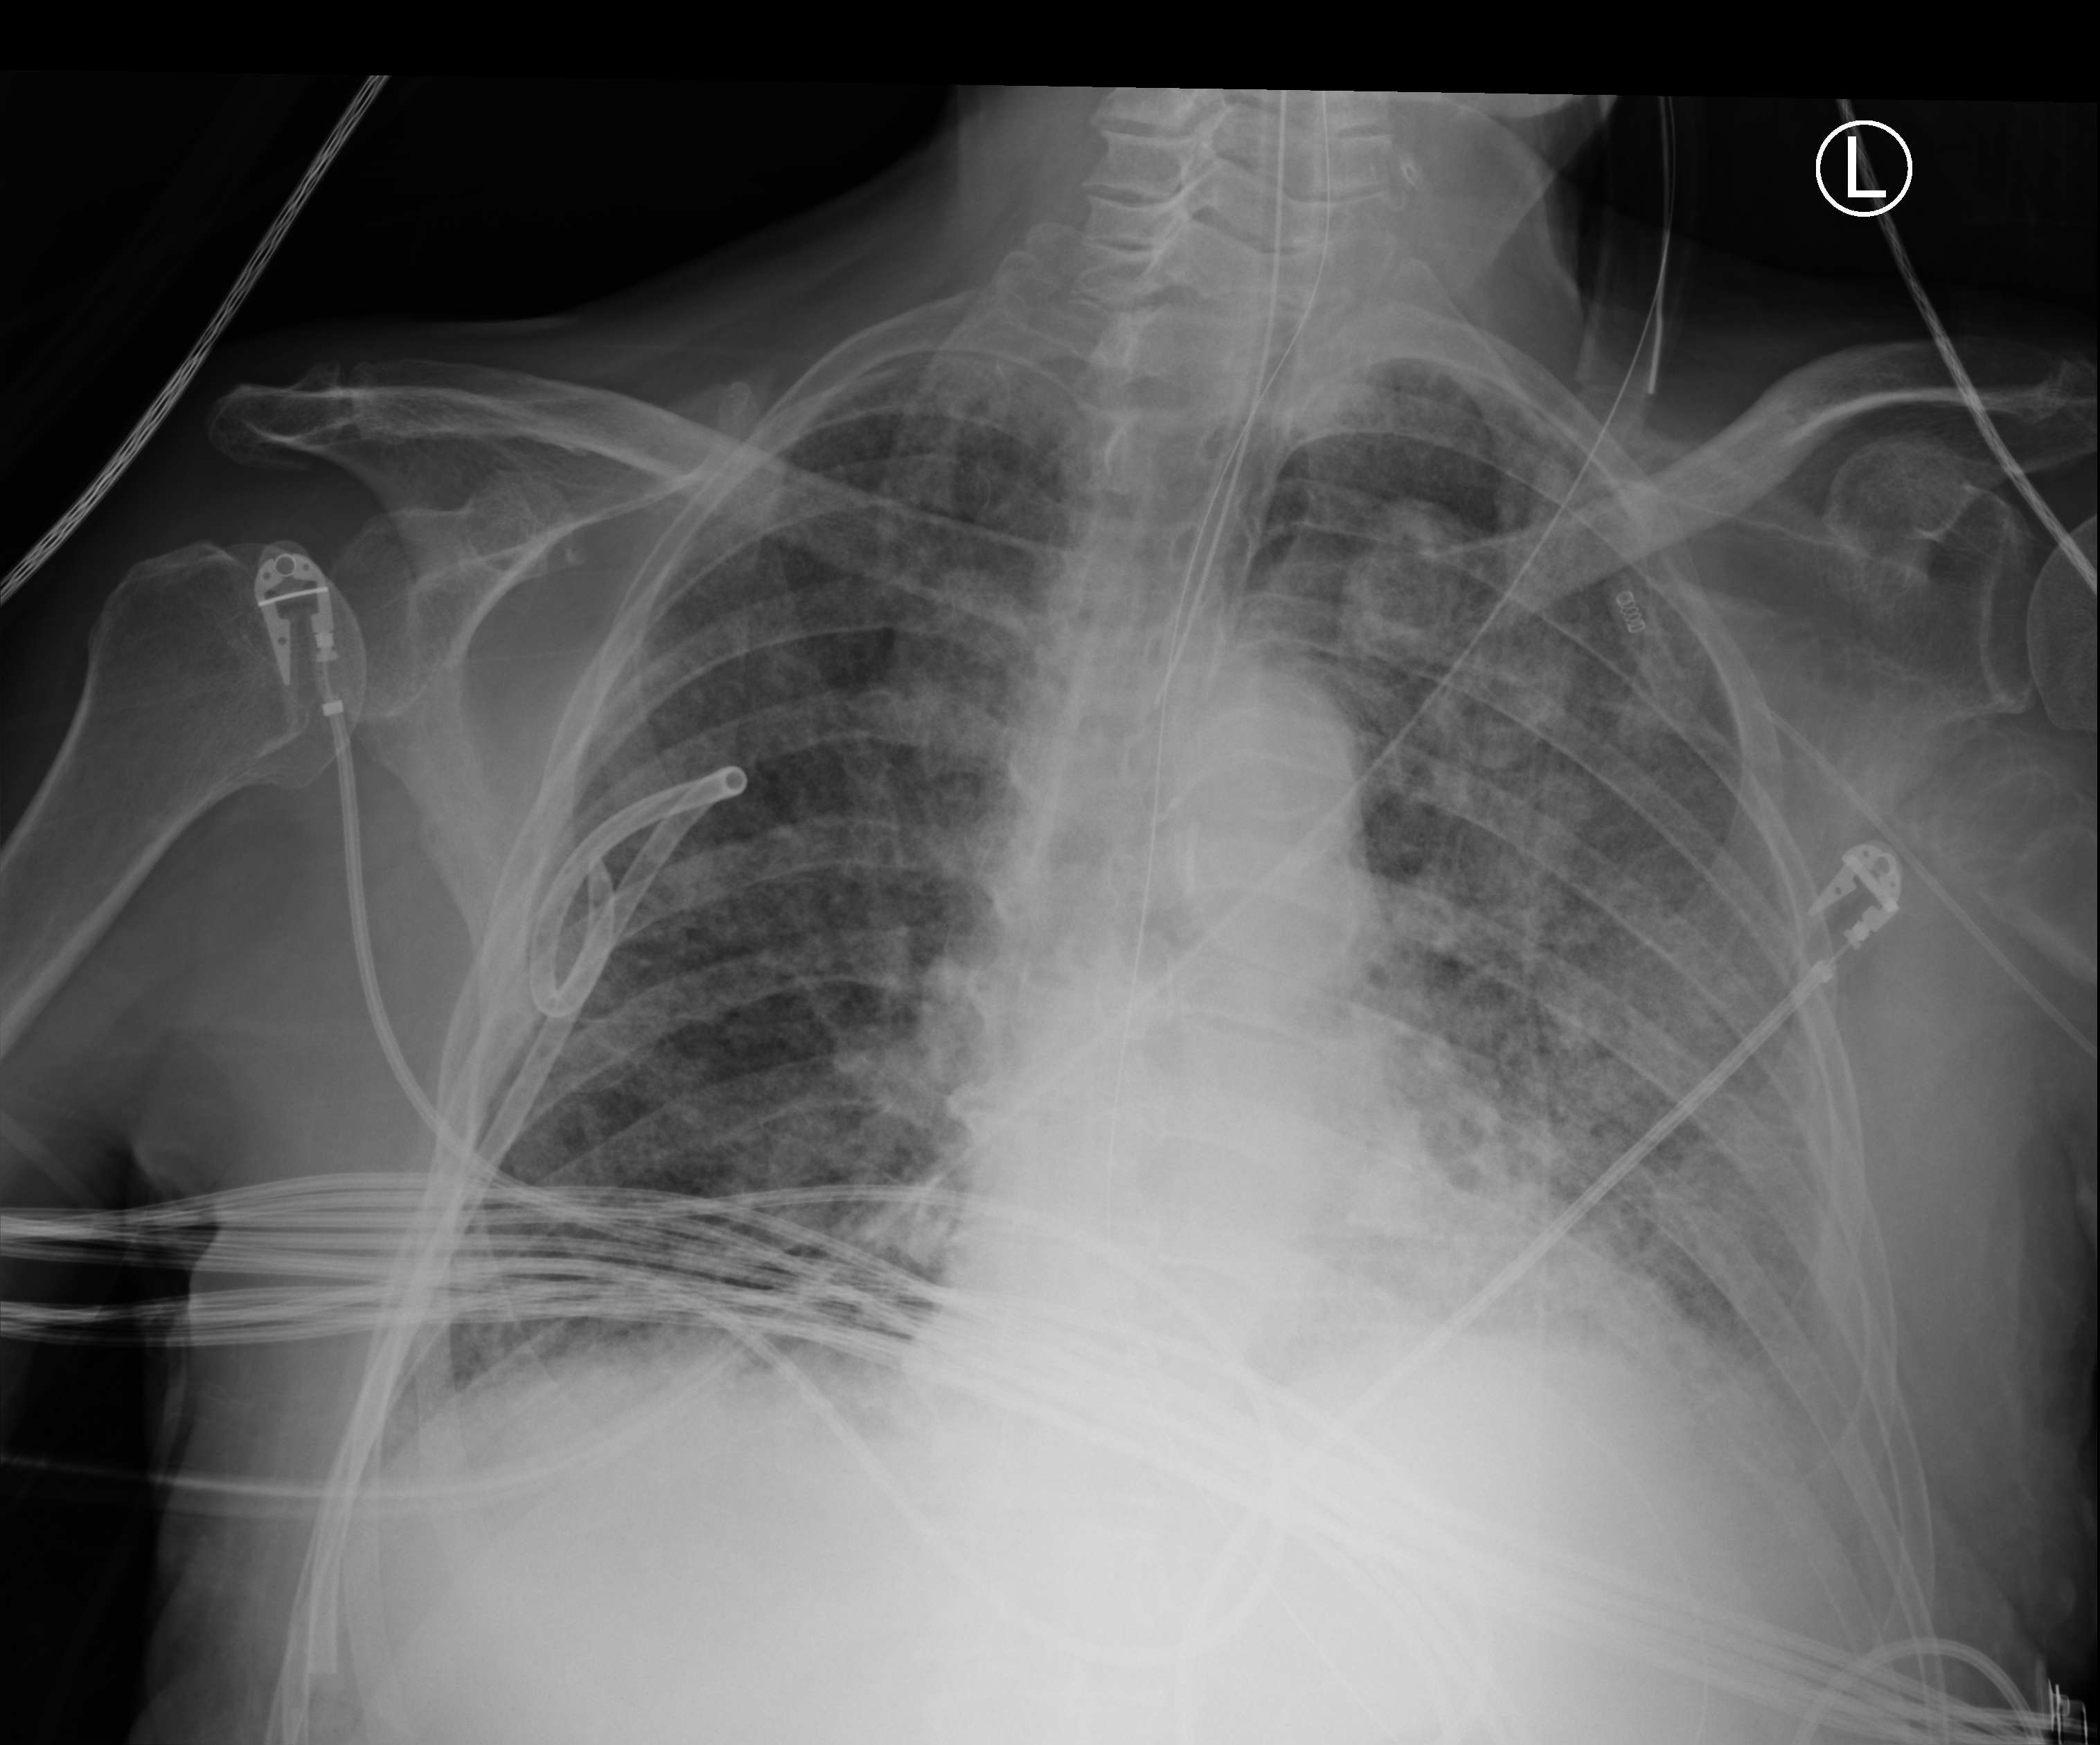
Portable chest radiograph, anteroposterior (AP) projection. Male patient hospitalised with COVID-19, age 75–90 years.
Admission-level facts for this patient (not findings on this image; timing relative to this image not recorded):
- length of hospital stay: 23 days
- mechanically ventilated during this hospital stay: yes
- admitted to intensive care during this hospital stay: yes